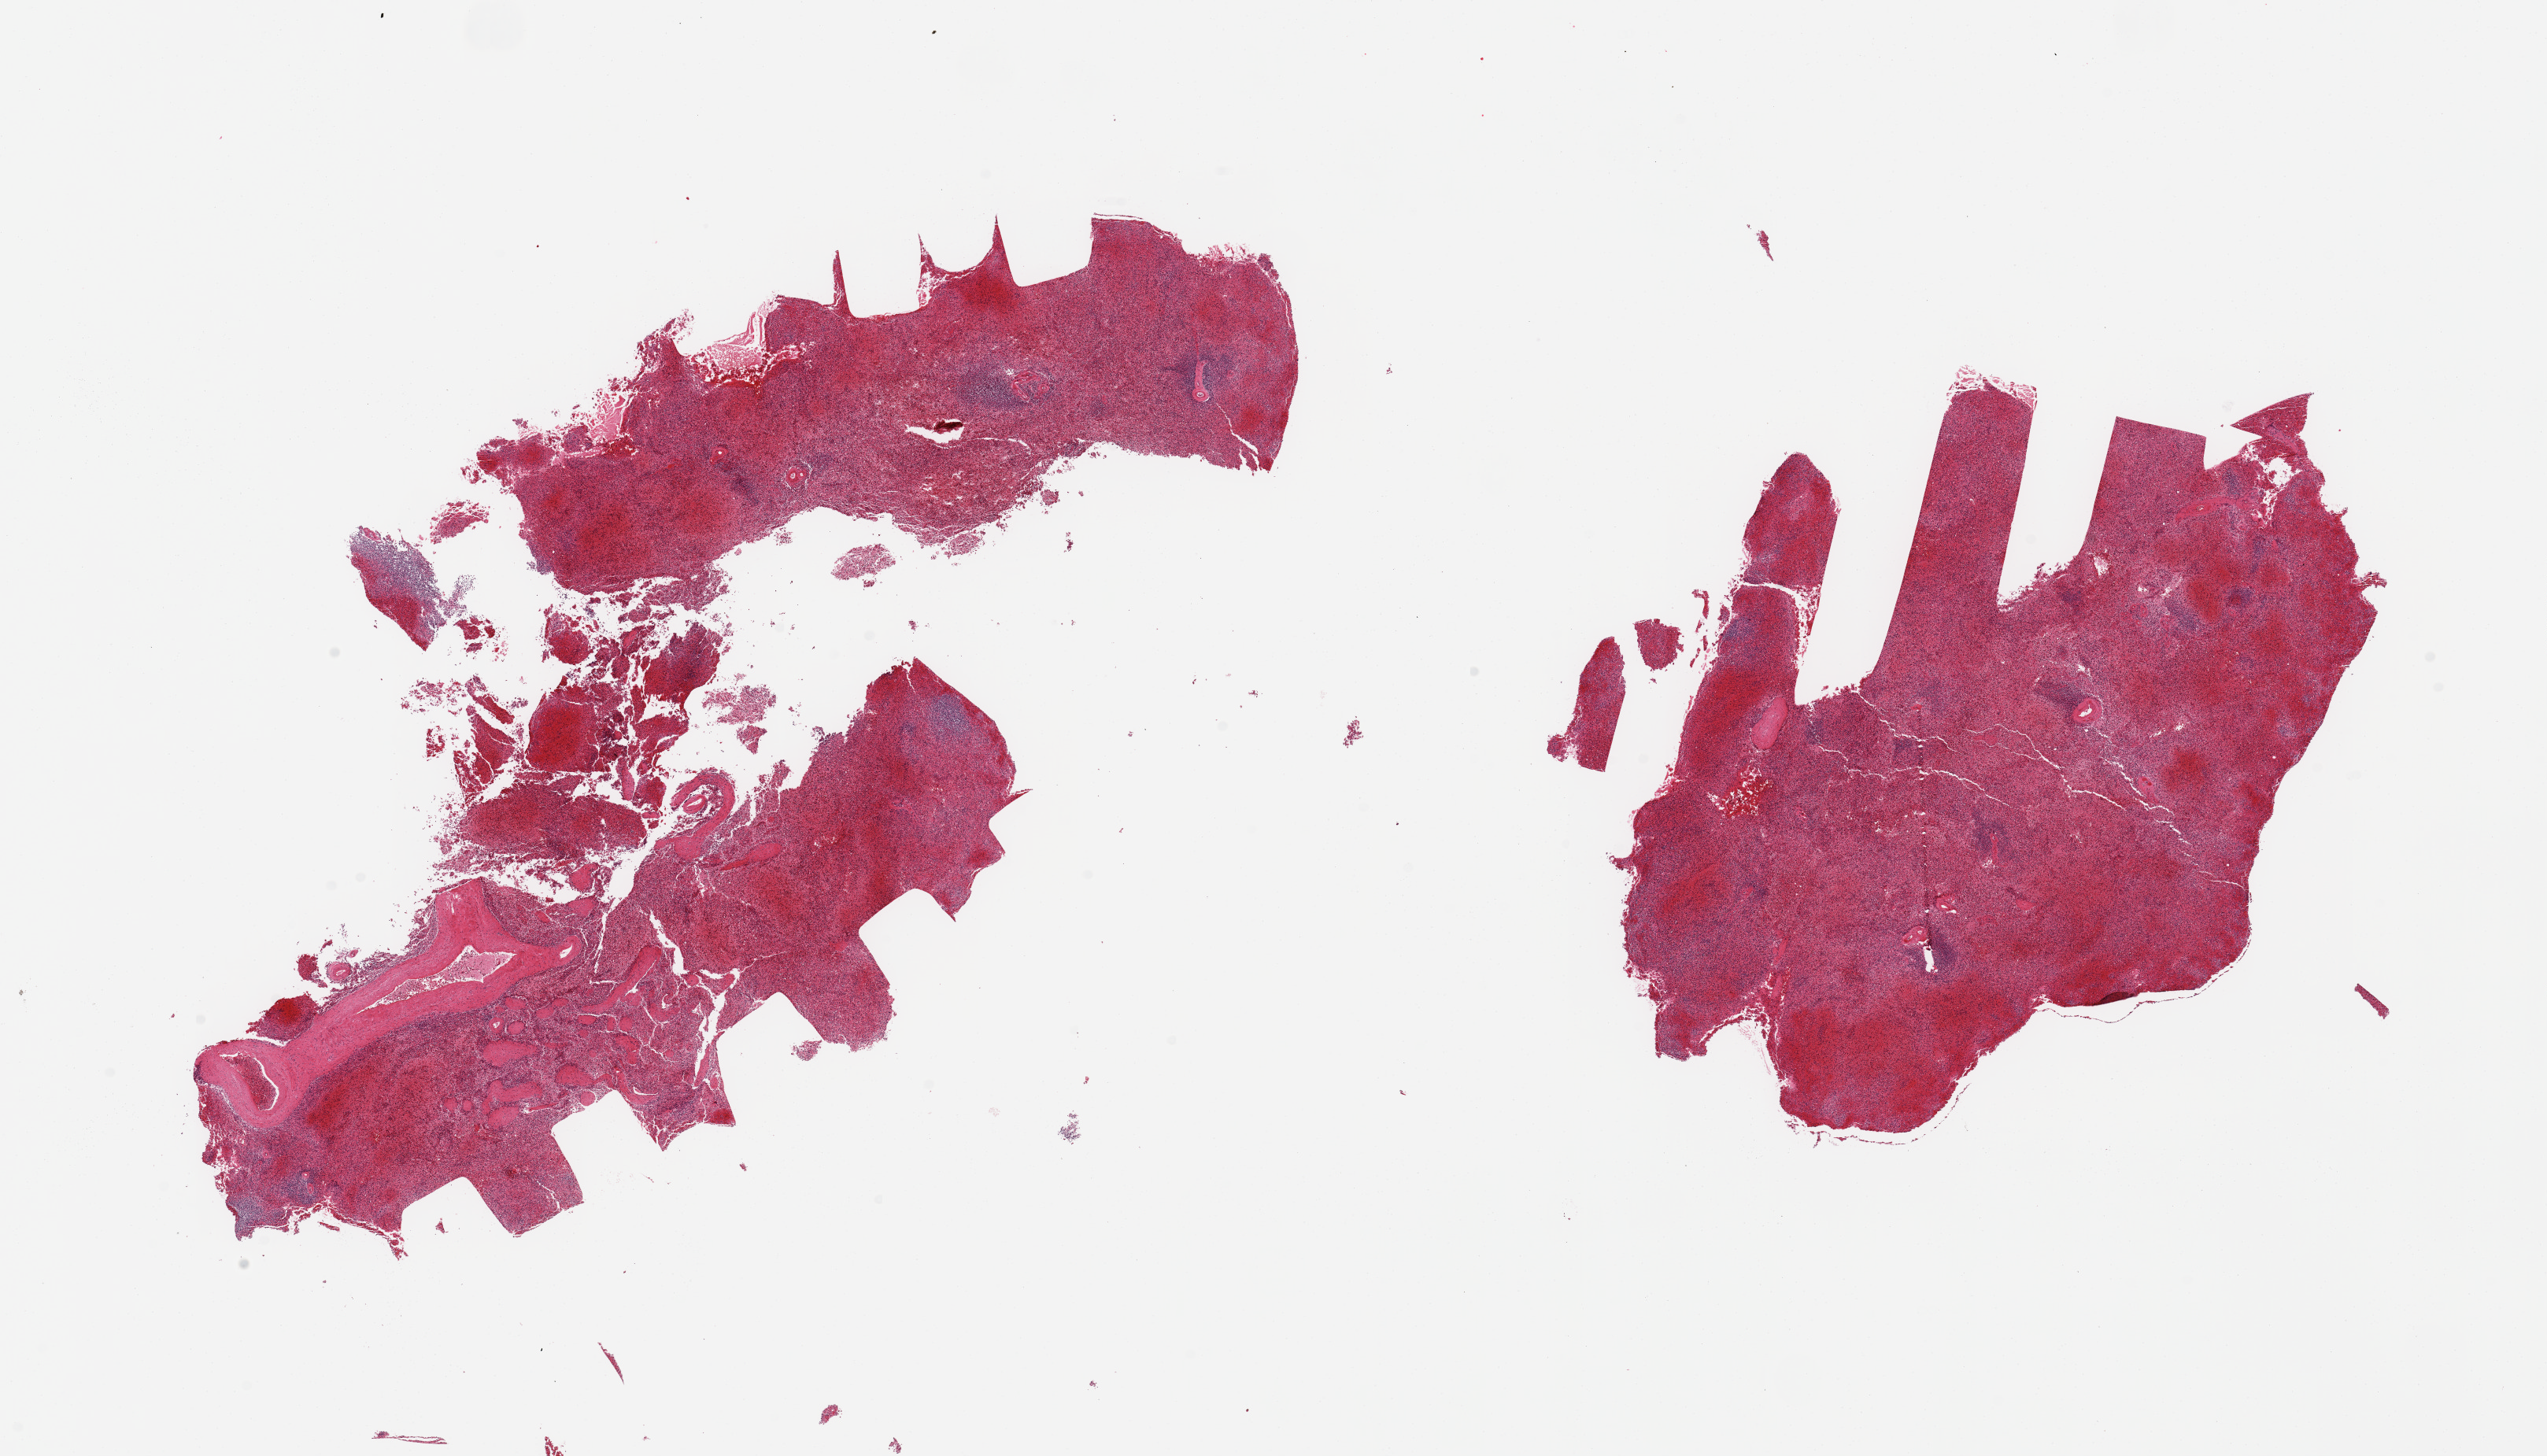
Whole-slide image, hematoxylin and eosin (H&E) stain, brightfield, a low-resolution overview of the entire scanned area, about 25.6 x 14.6 mm (from a 20x scan). PAXgene-fixed paraffin-embedded (PFPE) section. Target tissue: spleen. Donor tissue sample. Female donor.
* review note (as recorded): 2 pieces; congested